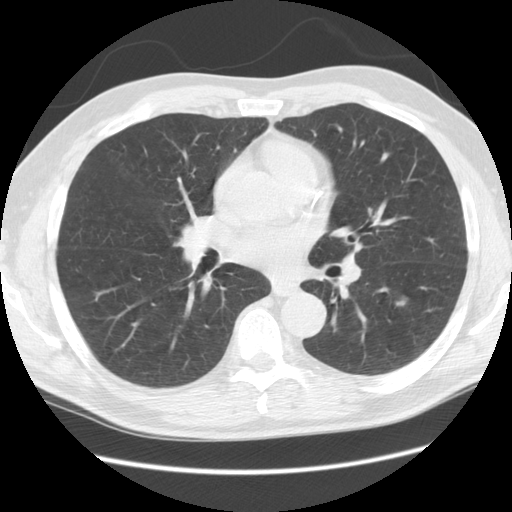
Low-dose screening chest CT, one axial slice. Position 54 of 111 along the scan axis. Reconstruction kernel STANDARD. Lung window (W 1500 / L -600 HU). 2.5 mm slice thickness. 512 × 512 image matrix, field of view 370 × 370 mm.
Annotated regions visible in this slice (manually delineated by an expert):
- lesion 1 (tumor, lower lobe of left lung): bounding box [x1, y1, x2, y2] px = [396, 298, 408, 307]